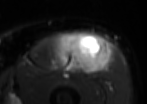
MRI of an extremity soft-tissue mass, one axial slice; position 43 of 85 along the scan axis; T2-weighted fat-saturated; MR volume resampled by the dataset authors to the PET/CT grid (not the native acquisition matrix); 147 × 104 image matrix. Male patient. Case-level facts recorded for this patient, not image findings: histological type: extraskeletal osteosarcoma; grade: high; site of the primary tumour: thigh.
Structures marked on this image (expert contour drawn on MRI and transferred to this co-registered scan by the dataset authors):
- gross tumour volume (mass): box from (x=58, y=31) to (x=107, y=73) px